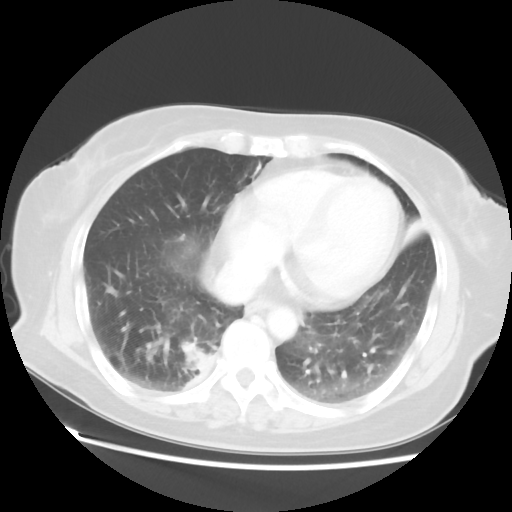
Chest CT, one axial slice; position 20 of 52 along the scan axis; reconstruction kernel STANDARD; lung window (W 1500 / L -600 HU); 5 mm slice thickness; 512 × 512 image matrix, field of view 356 × 356 mm. Female patient, age 69 years. From the clinical record (not read from this slice): clinical TNM (as recorded): T2 N1 M1a.
Outlined on this slice (bounding box drawn by a radiologist):
- lung tumour (recorded histology: adenocarcinoma): bounding box [x1, y1, x2, y2] px = [175, 337, 215, 388]